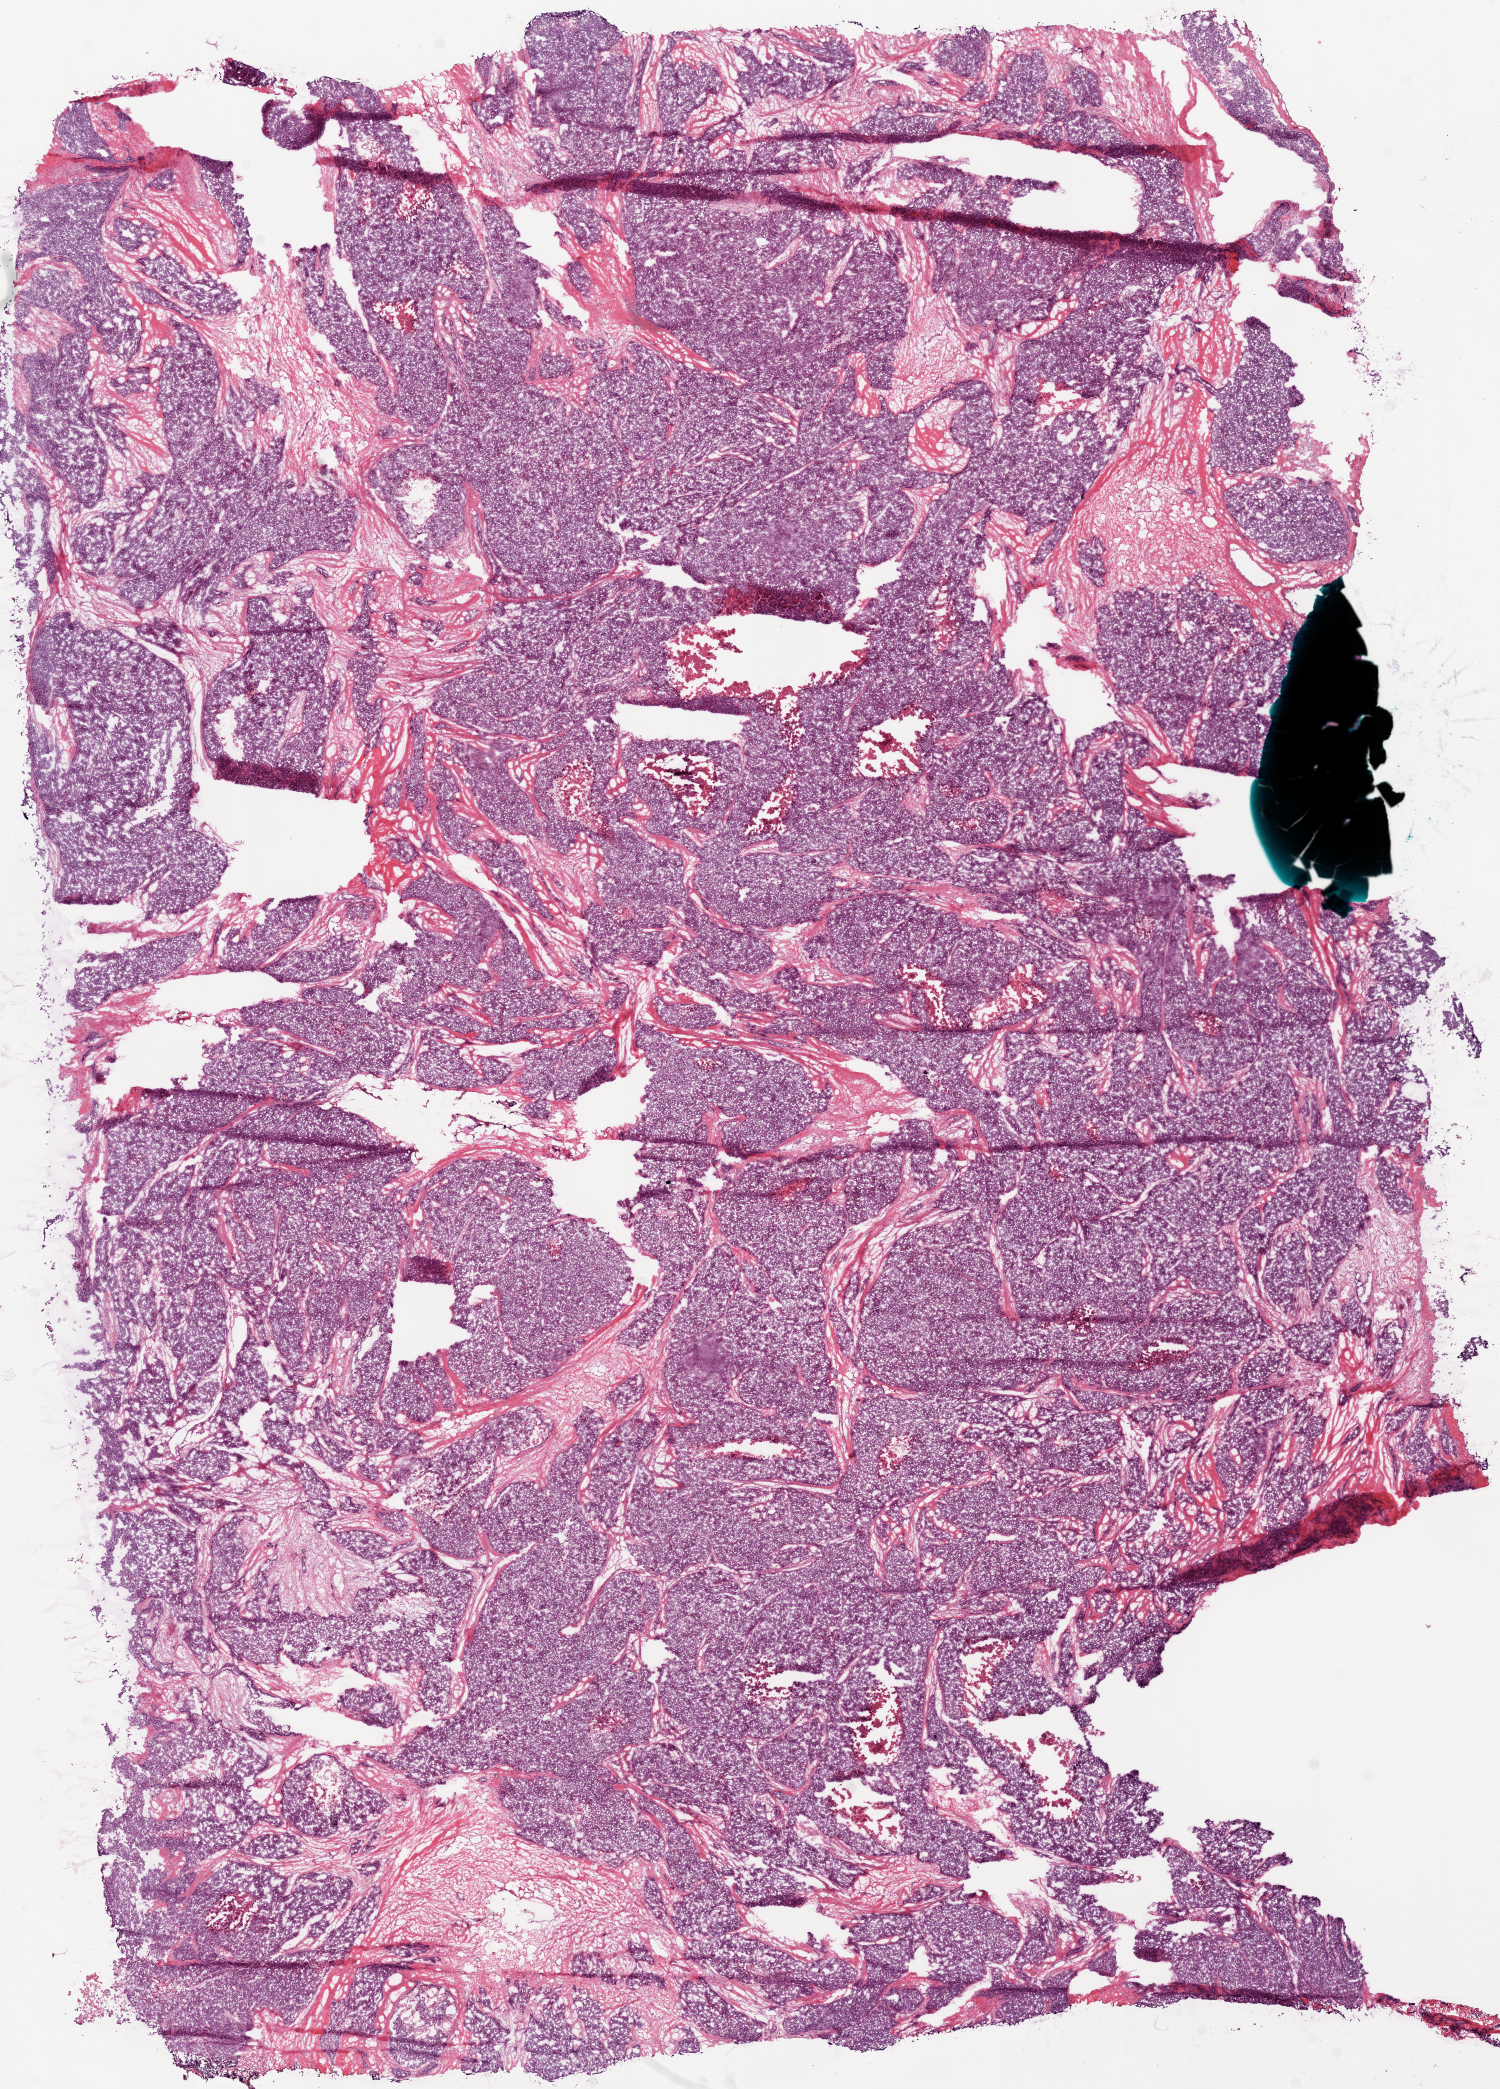
Digitized H&E tissue section (whole slide) — low-resolution overview of the scanned area, about 12.0 x 16.8 mm (from a 20x scan); frozen section from the bottom of the tissue portion; ovary, primary tumour sample. Female patient; age at initial diagnosis 73 years.
Diagnosis: Serous cystadenocarcinoma, NOS.